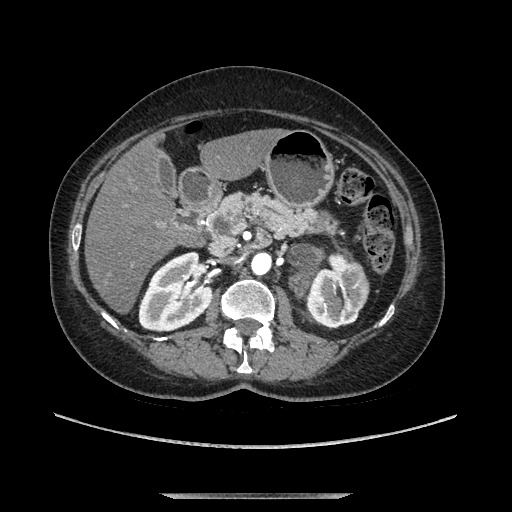
Contrast-enhanced abdominal CT, one axial slice. Slice 56 of 169 in the series (ordered by position). Soft-tissue window (W 400 / L 40 HU). 1.25 mm slice thickness. 512 × 512 image matrix, field of view 400 × 400 mm. Female patient. From the clinical record (not read from this slice): diagnosis: adrenocortical carcinoma; tumour side: left adrenal; tumour size at pathology: 9 cm; Ki-67 index: 2 %; stage (as recorded): 3.
Structures marked on this image (semi-automatic segmentation, software-assisted and operator-edited):
- mass: bounding box (x1, y1, x2, y2) in pixels: (290, 245, 324, 299)